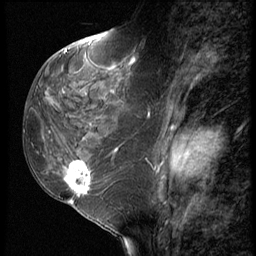
Breast MRI (dynamic contrast-enhanced), one sagittal slice; position 29 of 62 along the scan axis; 3 images stored at this slice position (order not interpretable as contrast timing); 1.5 T; TE 4.2 ms, TR 9 ms; 256 × 256 image matrix, field of view 180 × 180 mm. Patient: female, 50 years. From the clinical record (not read from this slice): setting: breast cancer imaged before/during neoadjuvant chemotherapy; receptor status: HR-positive, HER2-negative.
Annotated regions visible in this slice (semi-automatically segmented with operator editing):
- analysis volume of interest (the breast-tissue region the enhancement analysis was run in; not a lesion): box from (x=32, y=91) to (x=118, y=209) px
- tumour enhancement mask (voxels above the 140 % enhancement threshold inside the analysis volume of interest): (x=65, y=150)–(x=117, y=203)